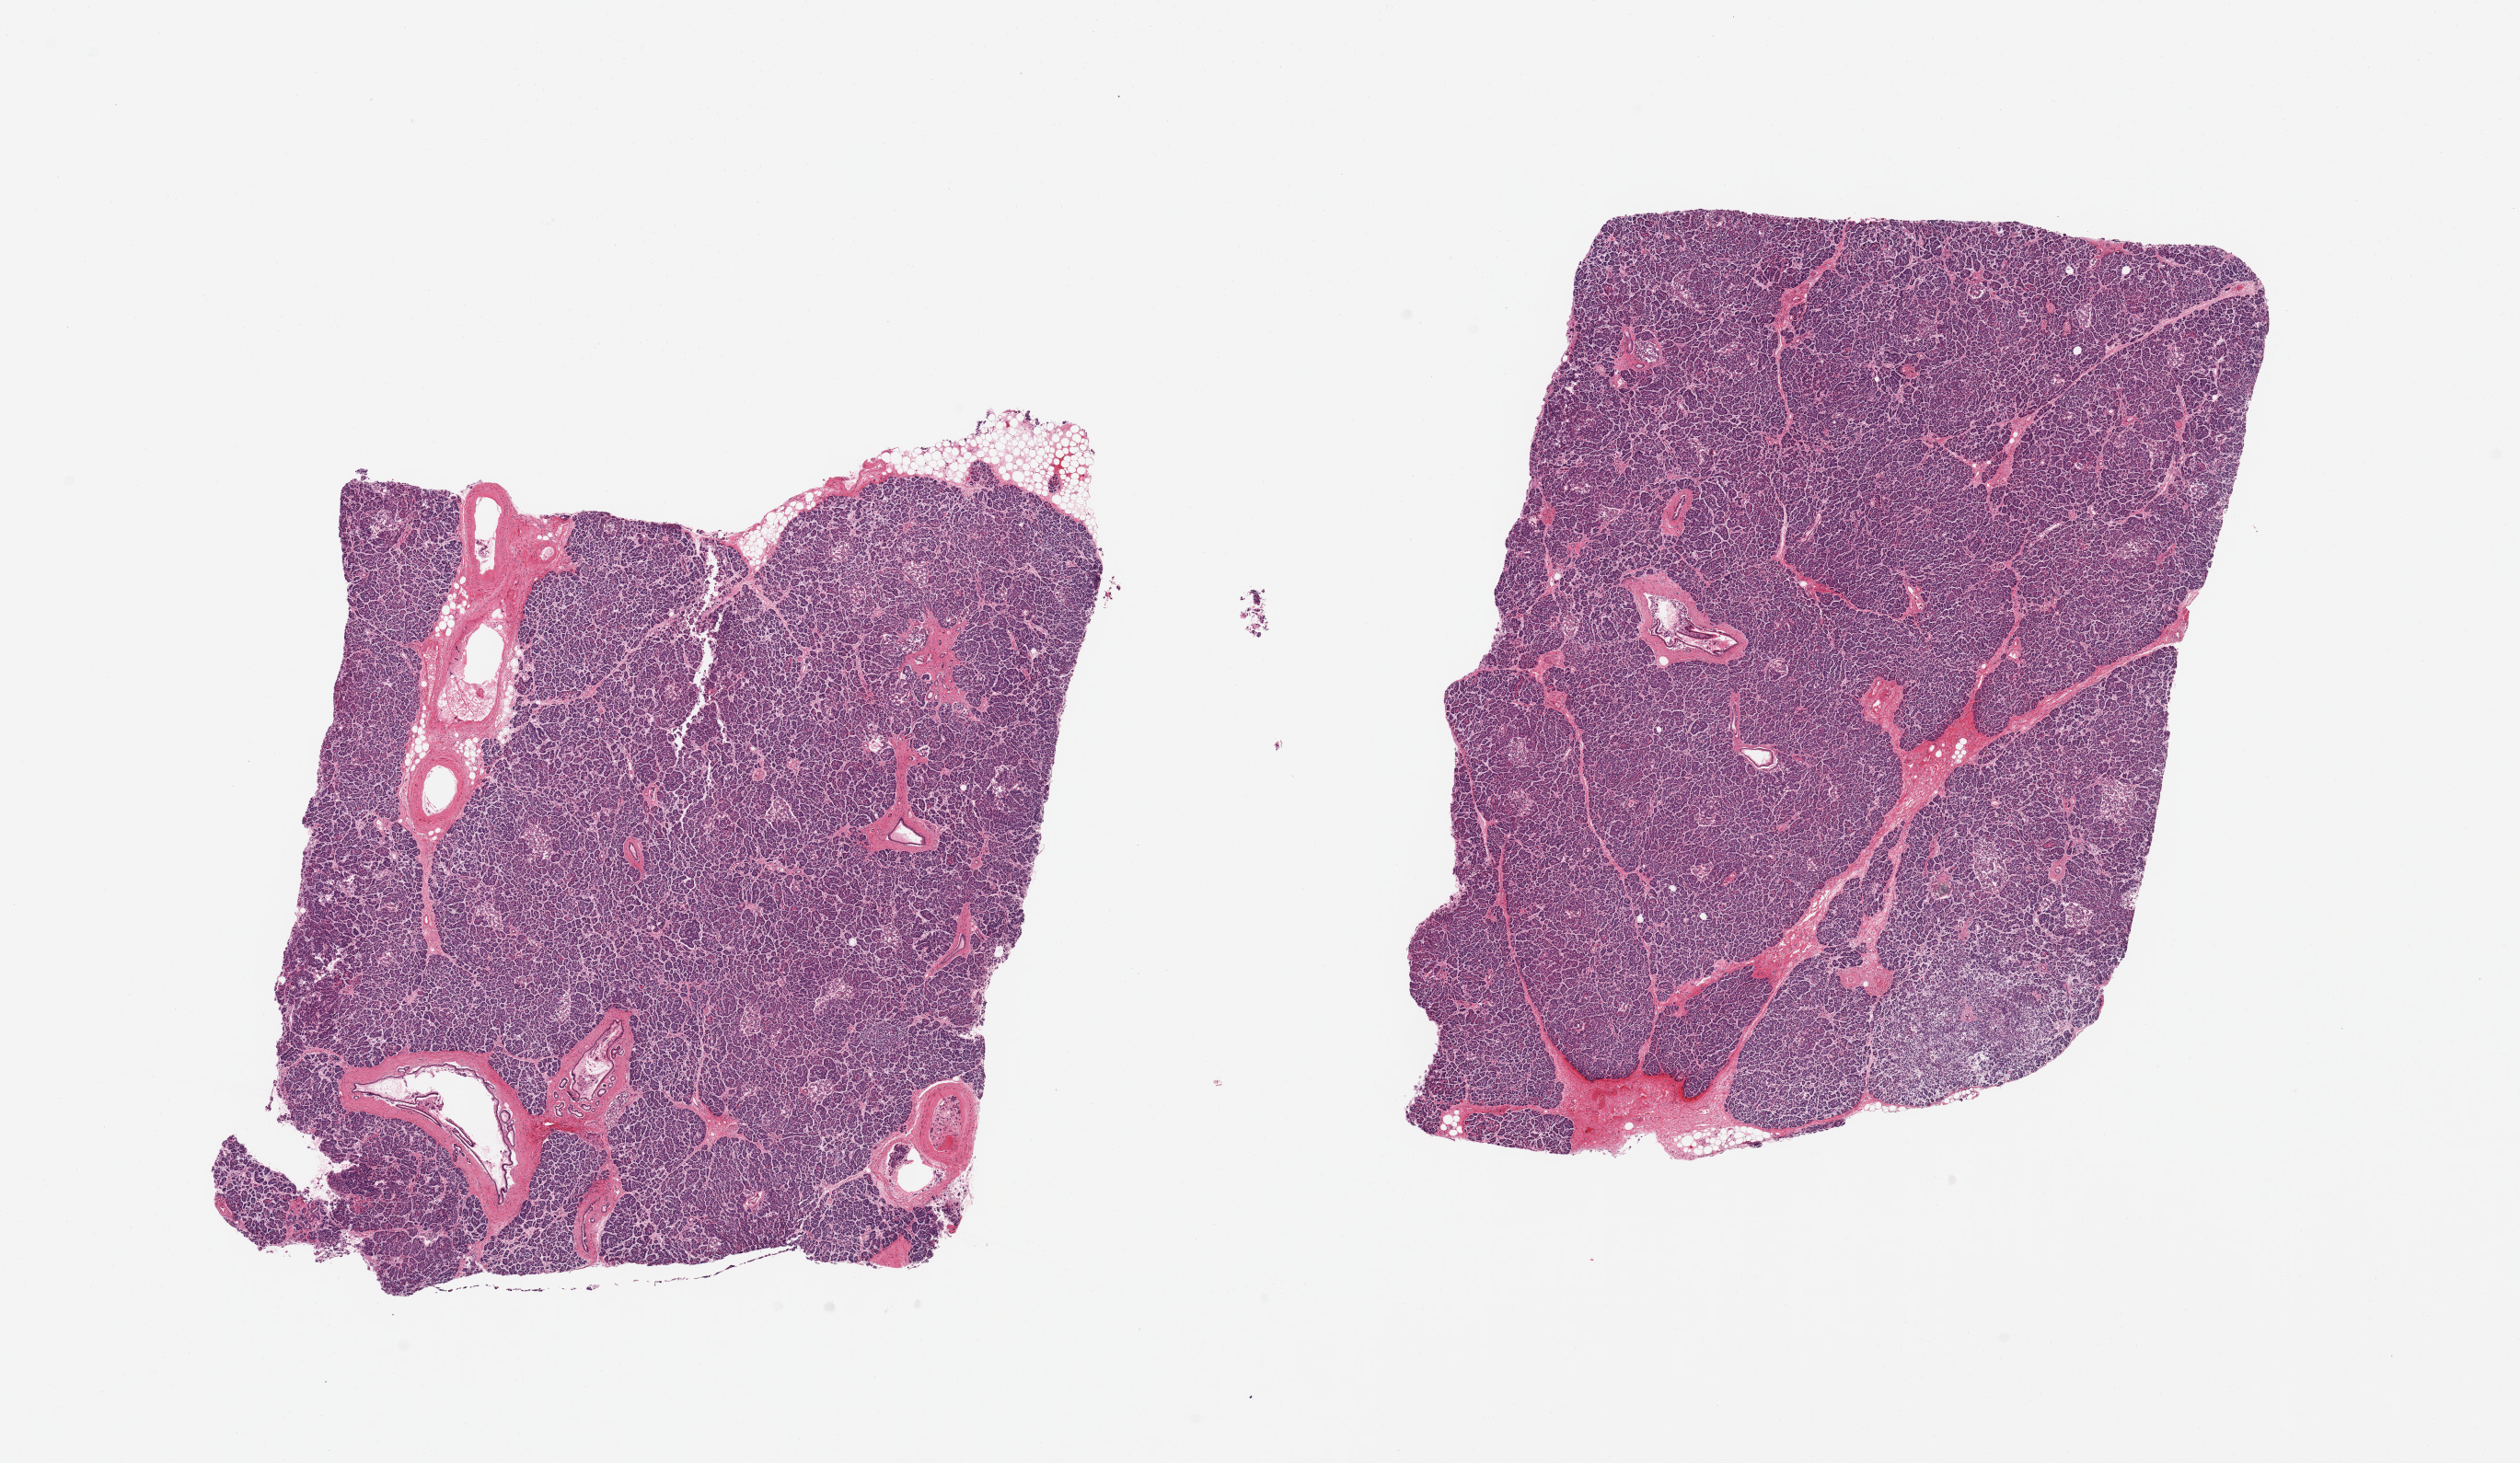
Hematoxylin and eosin (H&E) whole-slide image — whole scanned area (about 21.7 x 12.6 mm, acquisition: 20x scan) shown as a low-resolution overview; PAXgene-fixed, paraffin-embedded tissue; sampled site (target tissue): pancreas; tissue donor sample. Male donor.
Reviewer comment on this tissue sample: 2 pieces, Islets visible, just beginning to degrade.